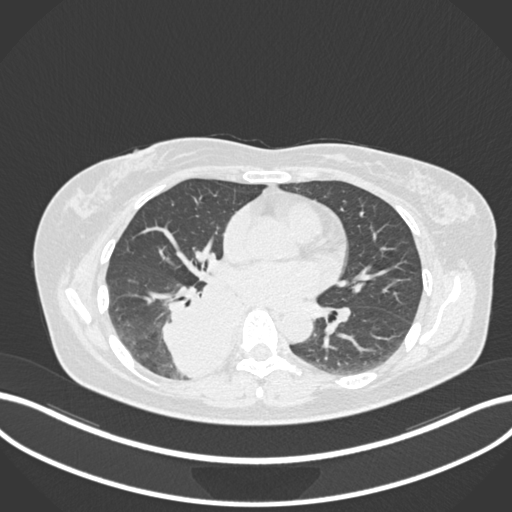
Chest CT, one axial slice. Position 582 of 677 along the scan axis. 120 kVp. Lung window (W 1500 / L -600 HU). 512 × 512 image matrix, field of view 400 × 400 mm. Female patient, age 54 years. From the clinical record (not read from this slice): clinical TNM (as recorded): T4 N0 M0.
Outlined on this slice (bounding box drawn by a radiologist):
- lung tumour (recorded histology: adenocarcinoma): box from (x=160, y=276) to (x=250, y=377) px